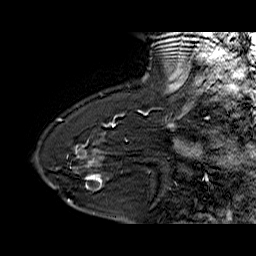
Breast MRI (dynamic contrast-enhanced), one sagittal slice. Slice 46 of 60 in the series (ordered by position). Dynamic contrast-enhanced series, time point 2 of 6 at this slice position (early post-contrast). 1.5 T. TE 6.4 ms, TR 32.9 ms. 256 × 256 image matrix, field of view 200 × 200 mm. Female patient. From the clinical record (not read from this slice): setting: breast cancer imaged before/during neoadjuvant chemotherapy; receptor status: HR-positive, HER2-negative.
Outlined on this slice (semi-automatically segmented with operator editing):
- analysis volume of interest (the breast-tissue region the enhancement analysis was run in; not a lesion): bounding box (x1, y1, x2, y2) in pixels: (68, 154, 125, 203)
- tumour enhancement mask (voxels above the 100 % enhancement threshold inside the analysis volume of interest): (68, 156, 102, 202)